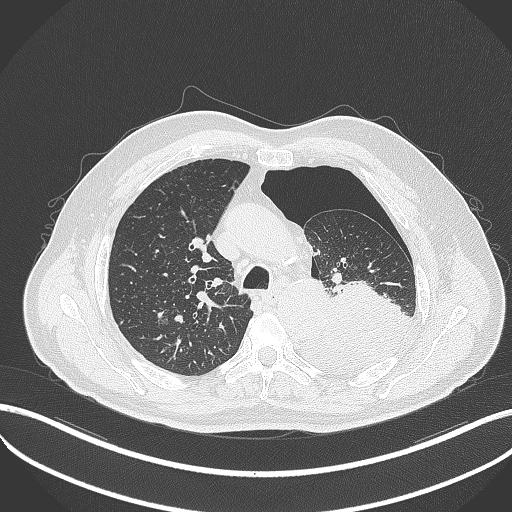
Chest CT, one axial slice. Slice 361 of 464 in the series (ordered by position). Reconstruction kernel B70f. 120 kVp. Lung window (W 1500 / L -600 HU). 1 mm slice thickness. 512 × 512 image matrix, field of view 400 × 400 mm. Male patient, age 76 years. From the clinical record (not read from this slice): clinical TNM (as recorded): T3 N0 M1b.
Outlined on this slice (rectangle marked by the reading radiologist):
- lung tumour (recorded histology: adenocarcinoma): bounding box (x1, y1, x2, y2) in pixels: (298, 278, 415, 374)